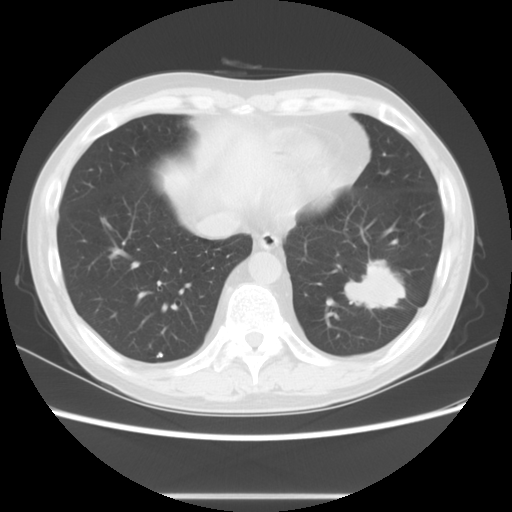
Chest CT, one axial slice. Slice 23 of 63 in the series (ordered by position). Reconstruction kernel STANDARD. Lung window (W 1500 / L -600 HU). 5 mm slice thickness. 512 × 512 image matrix. Male patient, age 49 years. Case-level facts recorded for this patient, not image findings: clinical TNM (as recorded): T3 N0 M0.
Structures marked on this image (bounding box drawn by a radiologist):
- lung tumour (recorded histology: squamous cell carcinoma): bounding box <339,250,412,321> (left, top, right, bottom; pixels)